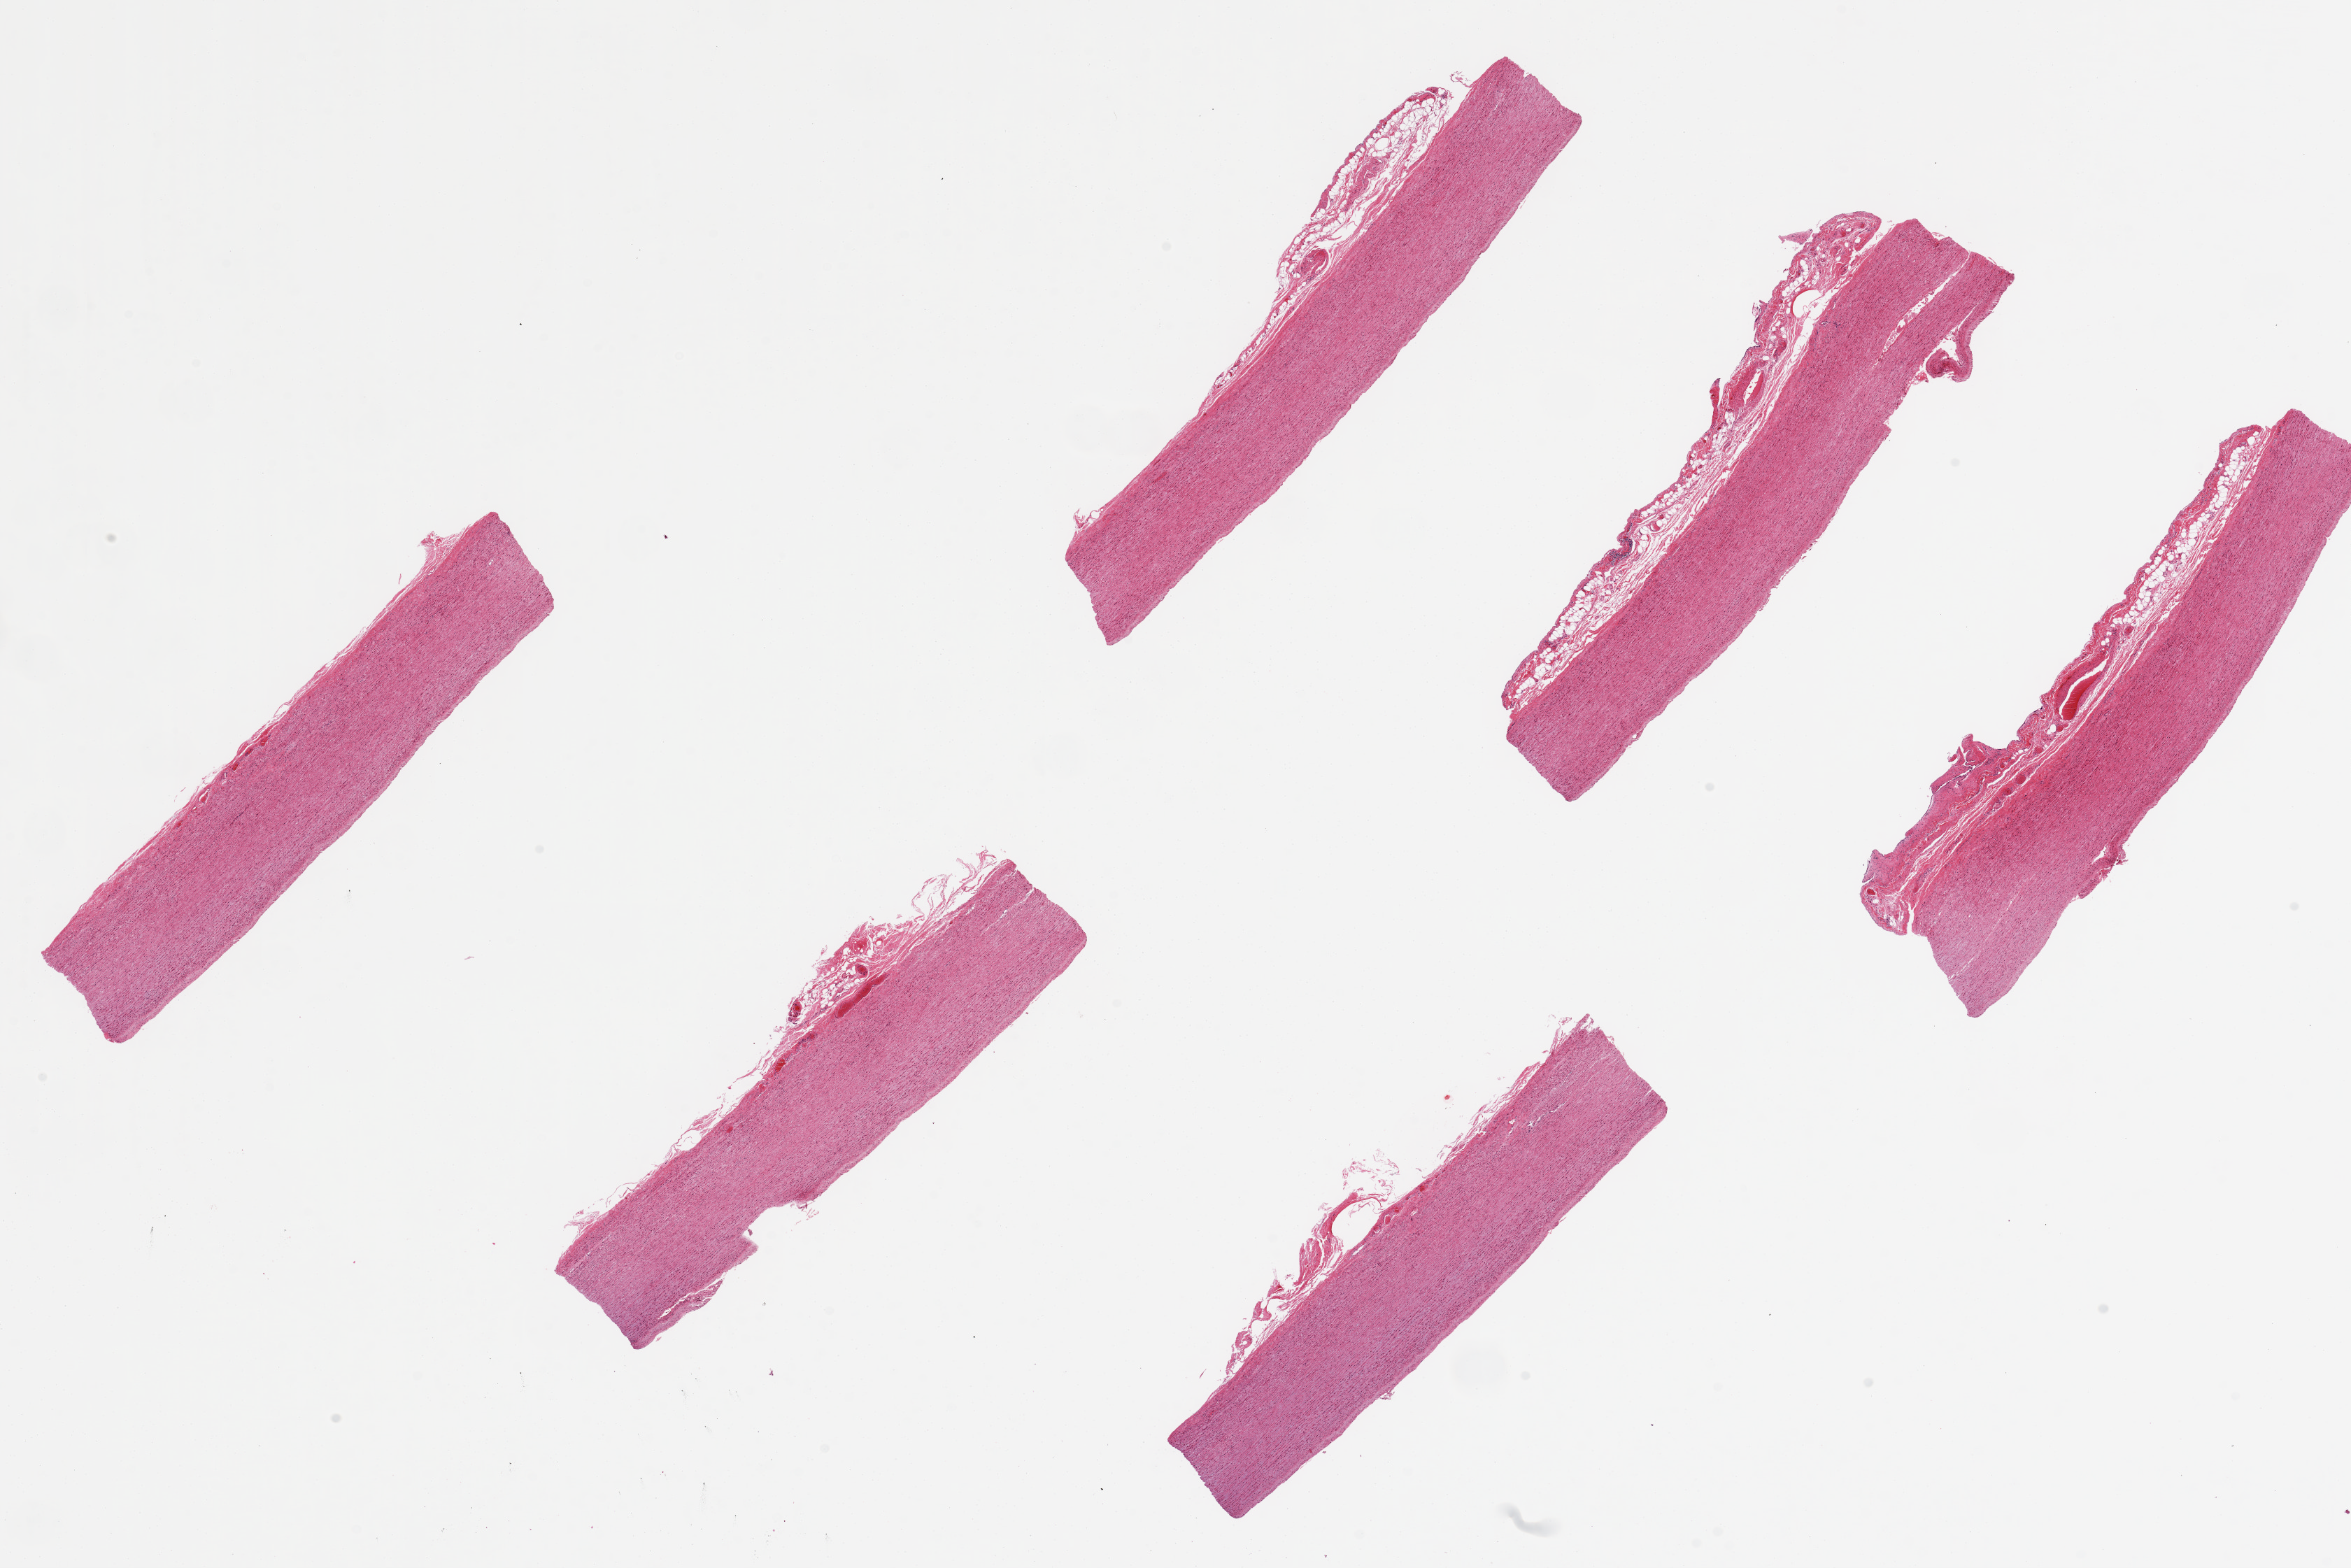
Haematoxylin and eosin whole-slide image, brightfield, shown as a low-resolution overview of the whole scanned area (about 26.6 x 17.7 mm, acquisition: 20x scan). PAXgene-fixed, paraffin-embedded tissue. Section of aorta (target tissue). Tissue donor sample. Donor: male.
- pathologist's review note for this sample: 6 pieces ~7x1.5mm